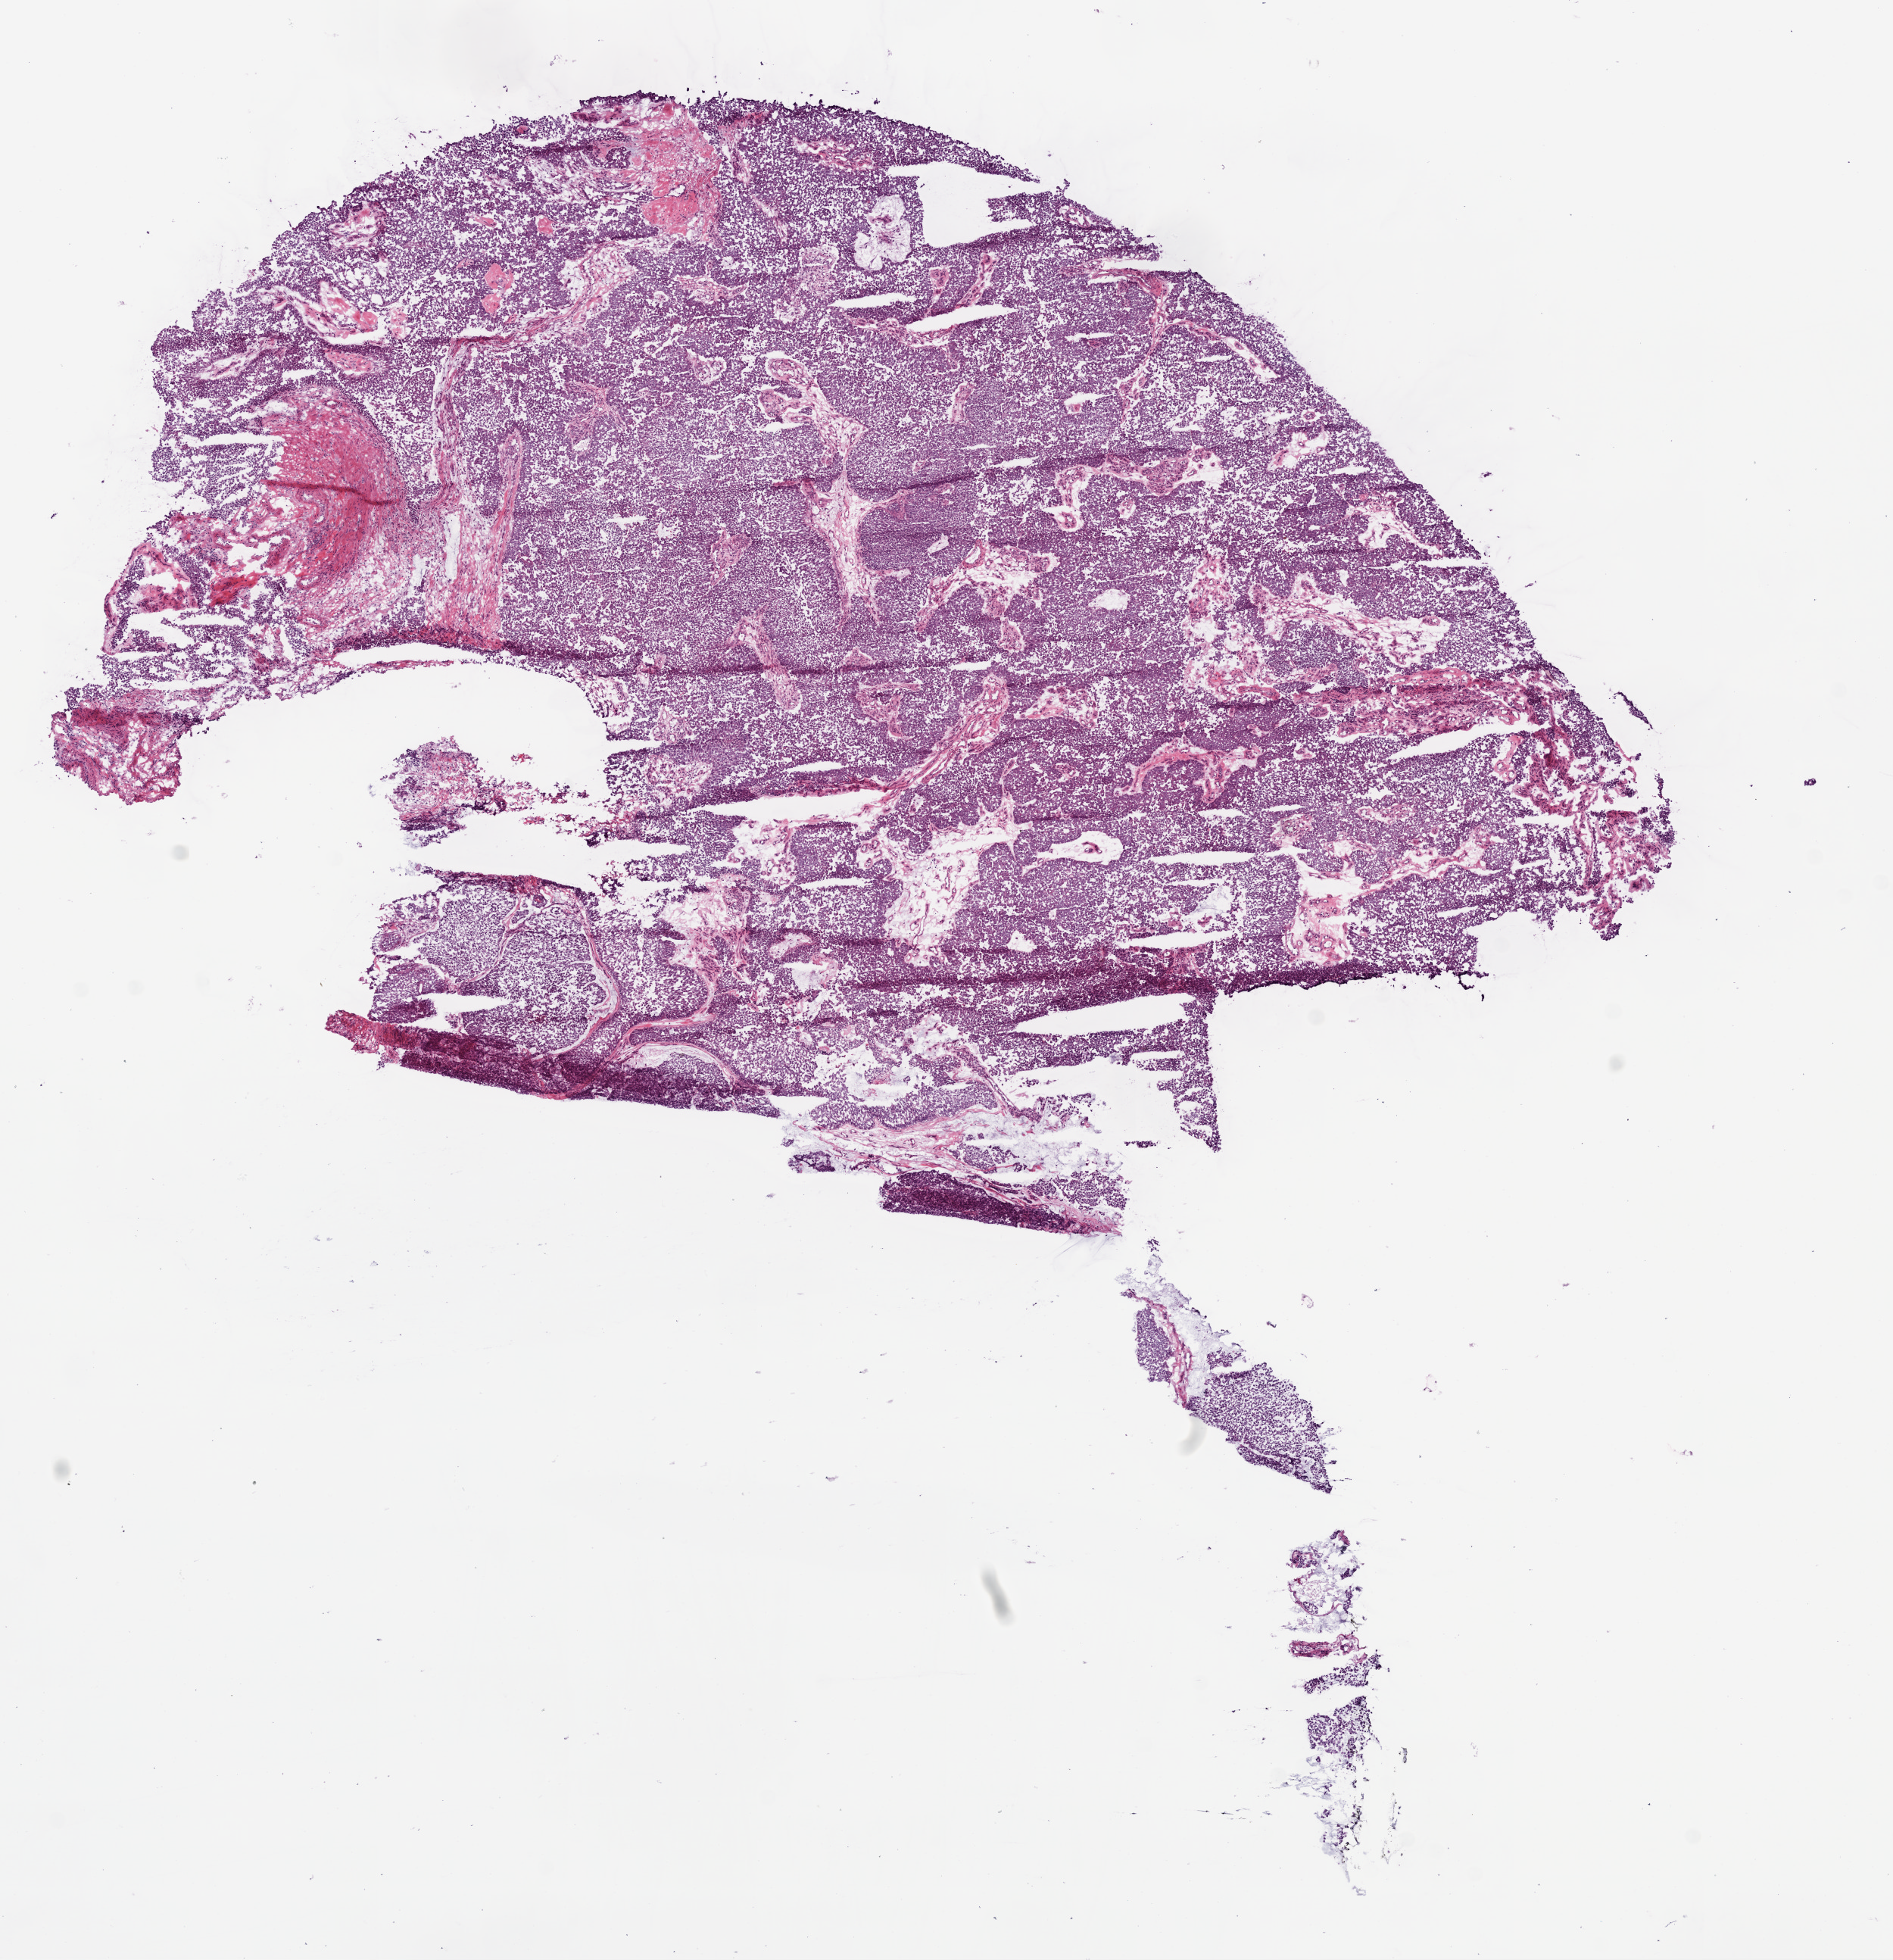
Digitized H&E-stained tissue section (whole slide) — low-resolution overview of the scanned area, about 10.0 x 10.4 mm (acquisition: 20x scan), frozen section from the bottom of the tissue portion, primary tumour sample from the kidney. Male, age 75 years at initial diagnosis. Pathologist review of this section (percent, as recorded): tumour cells 85%, tumour nuclei 85%, normal cells 0%, stromal cells 10%, necrosis 5%.
TNM: T2 NX M0. AJCC pathologic stage: II. Diagnosis: Papillary adenocarcinoma, NOS.